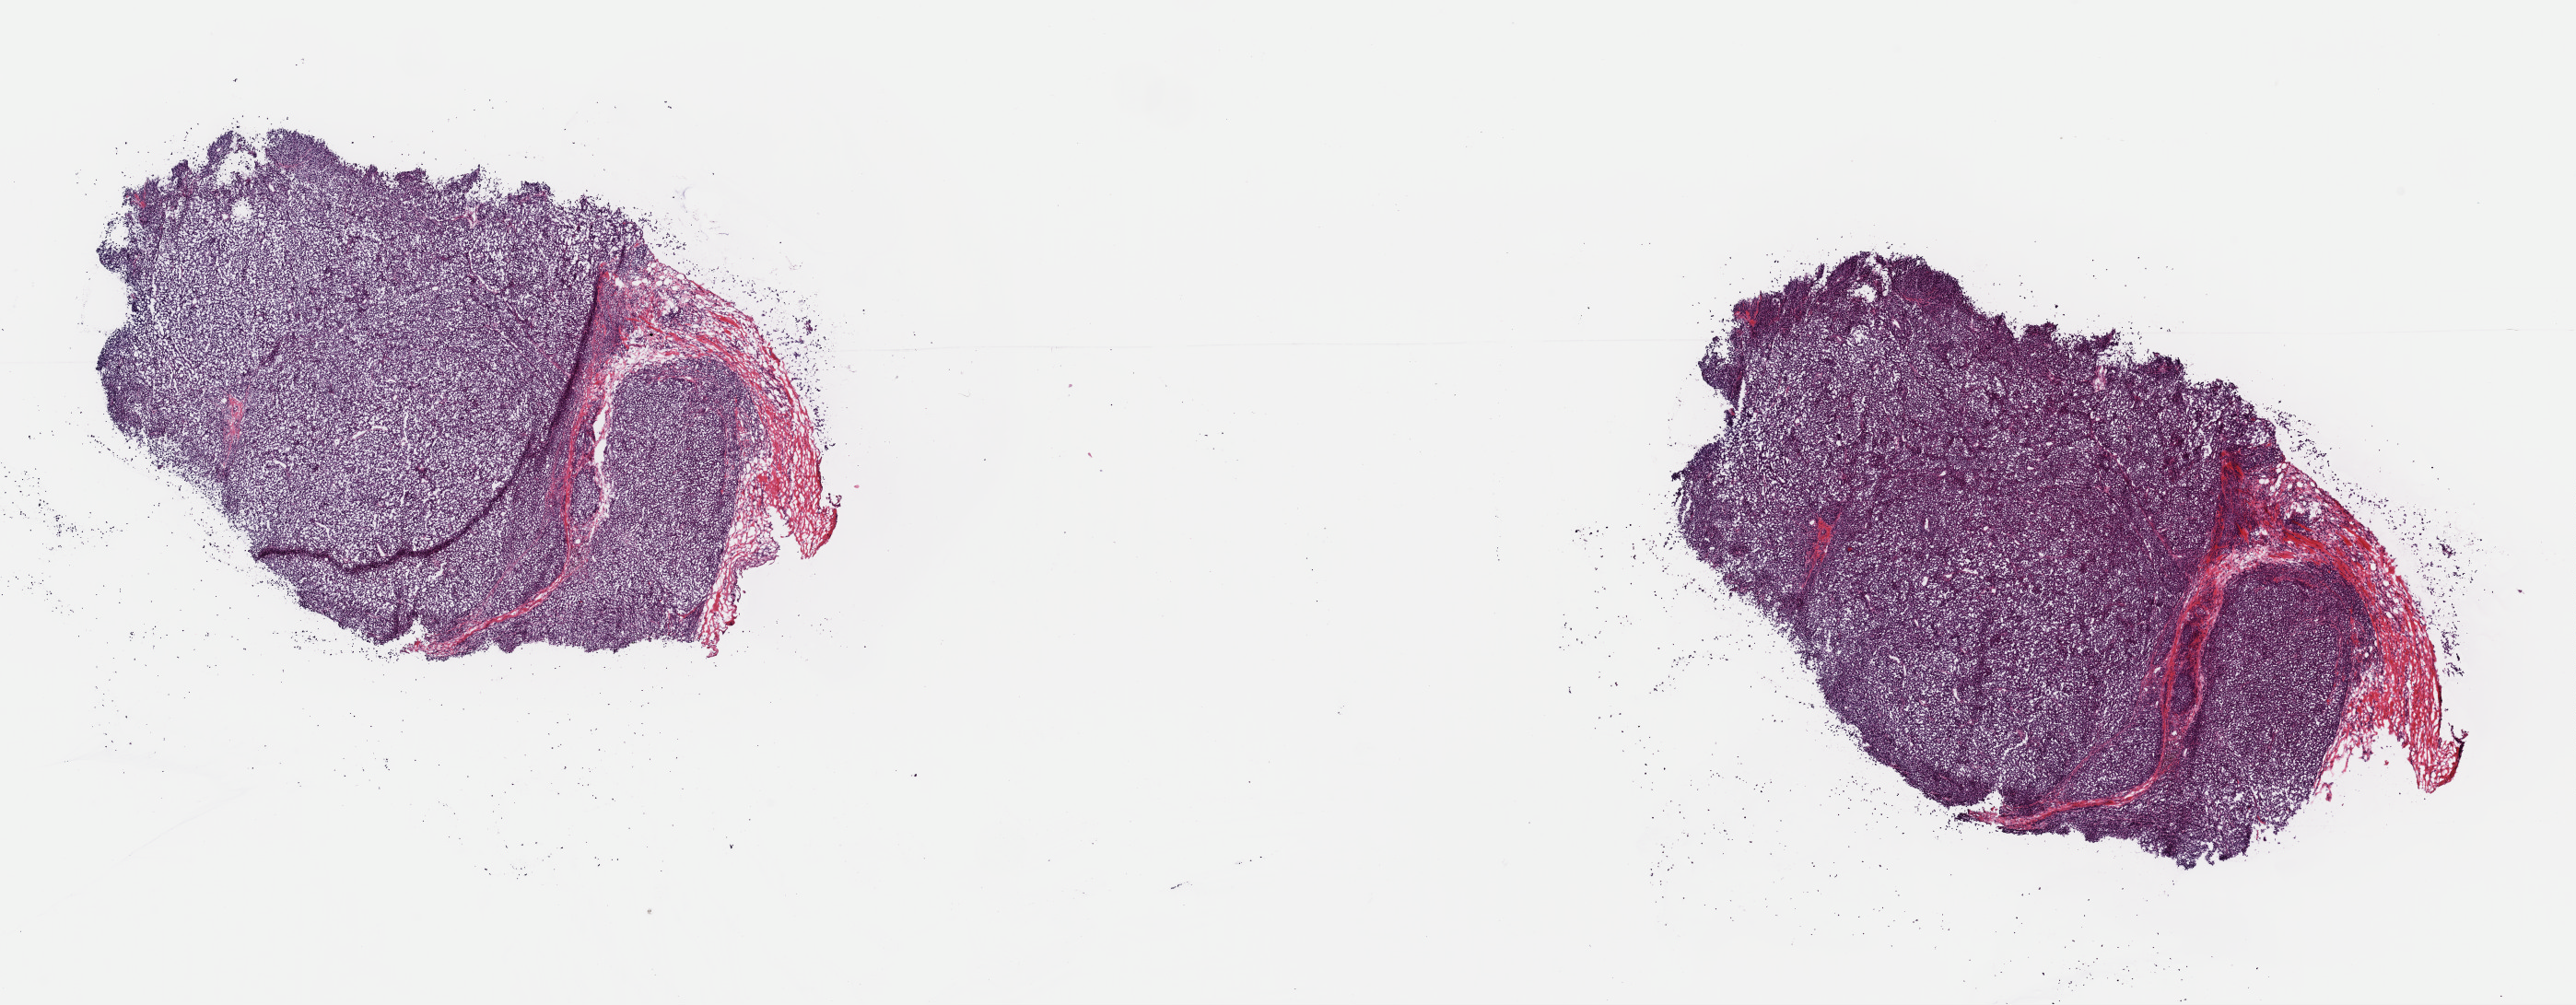
Digitized H&E tissue section (whole slide) — shown as a low-resolution overview of the whole scanned area (about 22.1 x 8.6 mm, slide scanned at 40x). Frozen section. Metastatic tumour sample, sampled site: lymph nodes of head, face and neck. Male, age 52 years at initial diagnosis. Slide review estimates, as recorded: tumour cells 80%, tumour nuclei 80%, normal cells 0%, stromal cells 20%, necrosis 0%. Infiltration values recorded for this section: lymphocyte infiltration 5%, monocyte infiltration 0%, neutrophil infiltration 0%.
This section: metastatic tumour tissue. Patient diagnosis: Malignant melanoma, NOS.